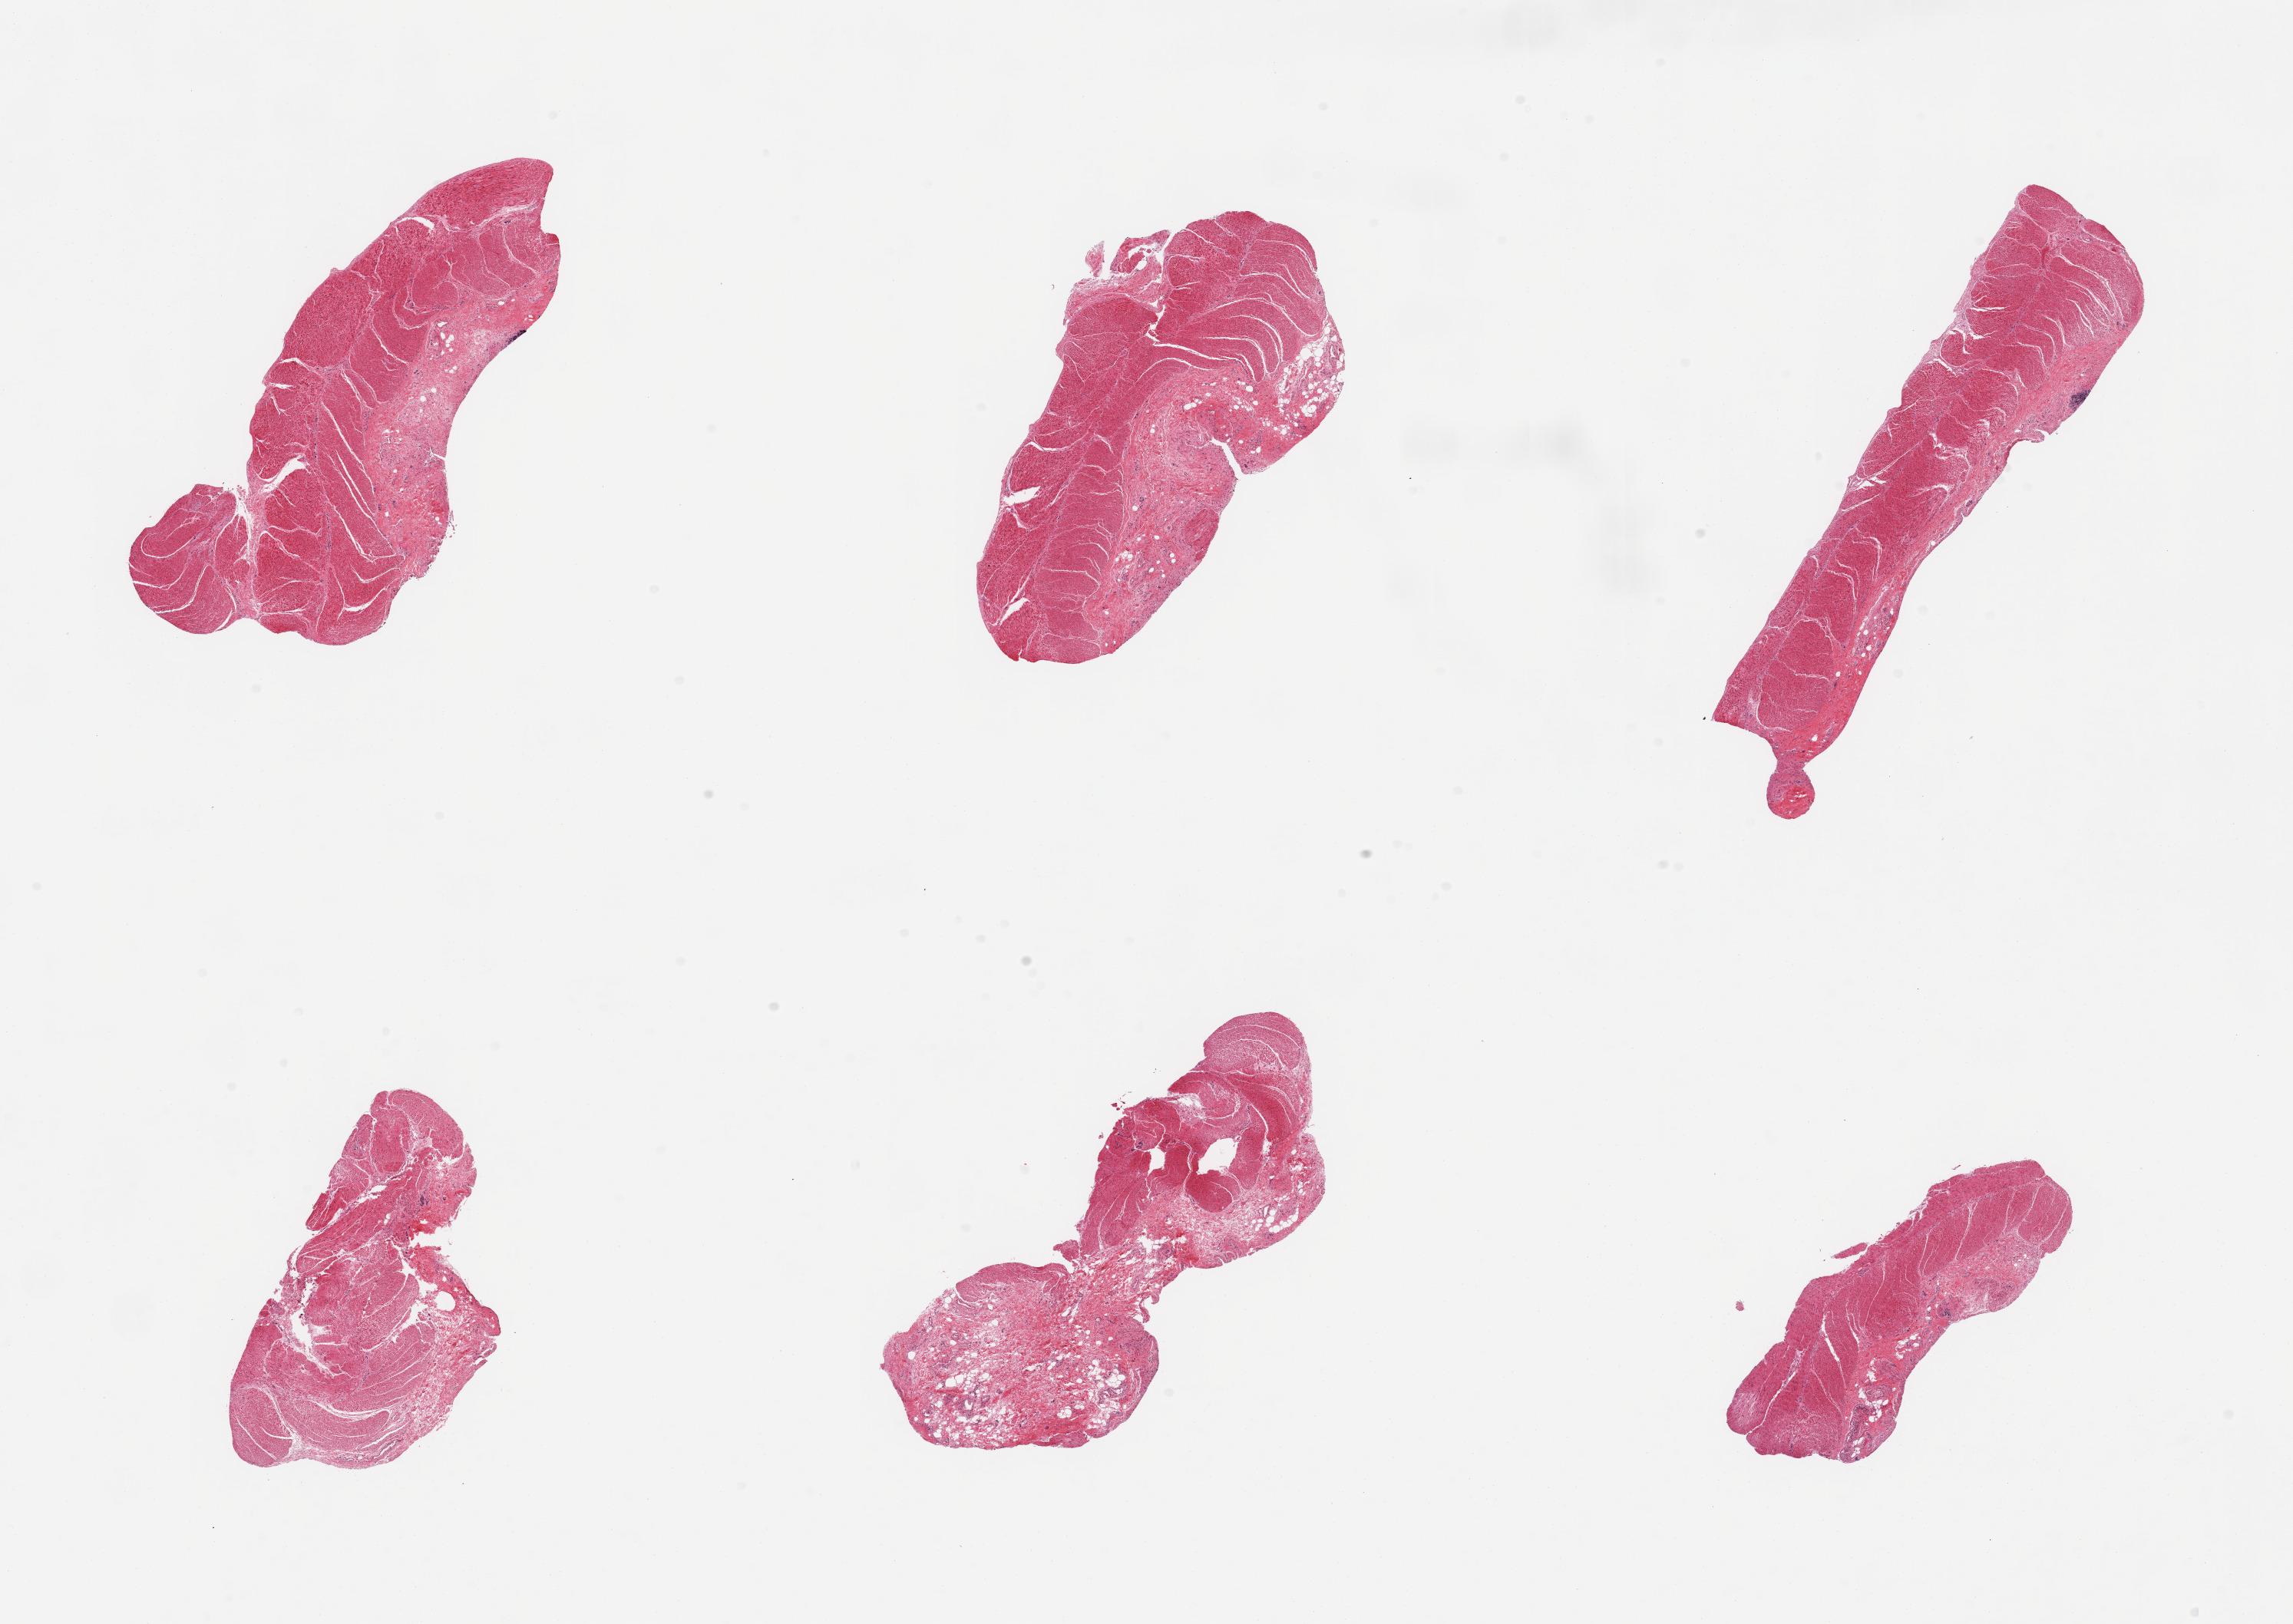
Haematoxylin and eosin whole-slide image — a low-resolution overview of the entire scanned area, about 23.6 x 16.7 mm. PAXgene-fixed paraffin-embedded (PFPE) section. Sampled site (target tissue): sigmoid colon. Donor tissue sample. Donor: female.
- pathologist's review note for this sample: 6 pieces; muscularis propria with varying amounts of fibrofatty stroma